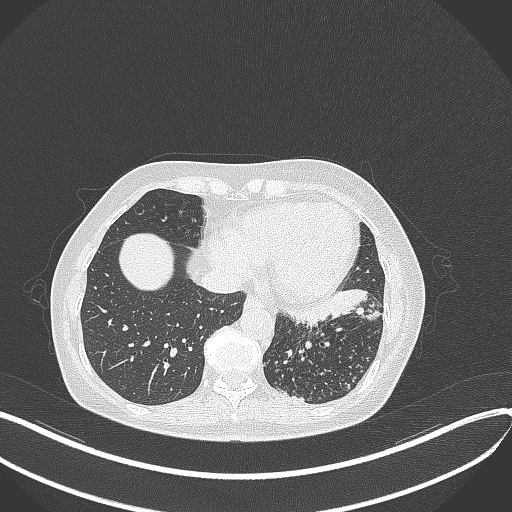
Chest CT, one axial slice. Slice 120 of 429 in the series (ordered by position). Reconstruction kernel B70f. 100 kVp. Lung window (W 1500 / L -600 HU). 1 mm slice thickness. 512 × 512 image matrix, field of view 400 × 400 mm. Female patient, age 63 years. From the clinical record (not read from this slice): clinical TNM (as recorded): T1b N0 M0; histopathological grade: G2-3.
Outlined on this slice (bounding box drawn by a radiologist):
- lung tumour (recorded histology: adenocarcinoma): box from (x=288, y=289) to (x=384, y=328) px